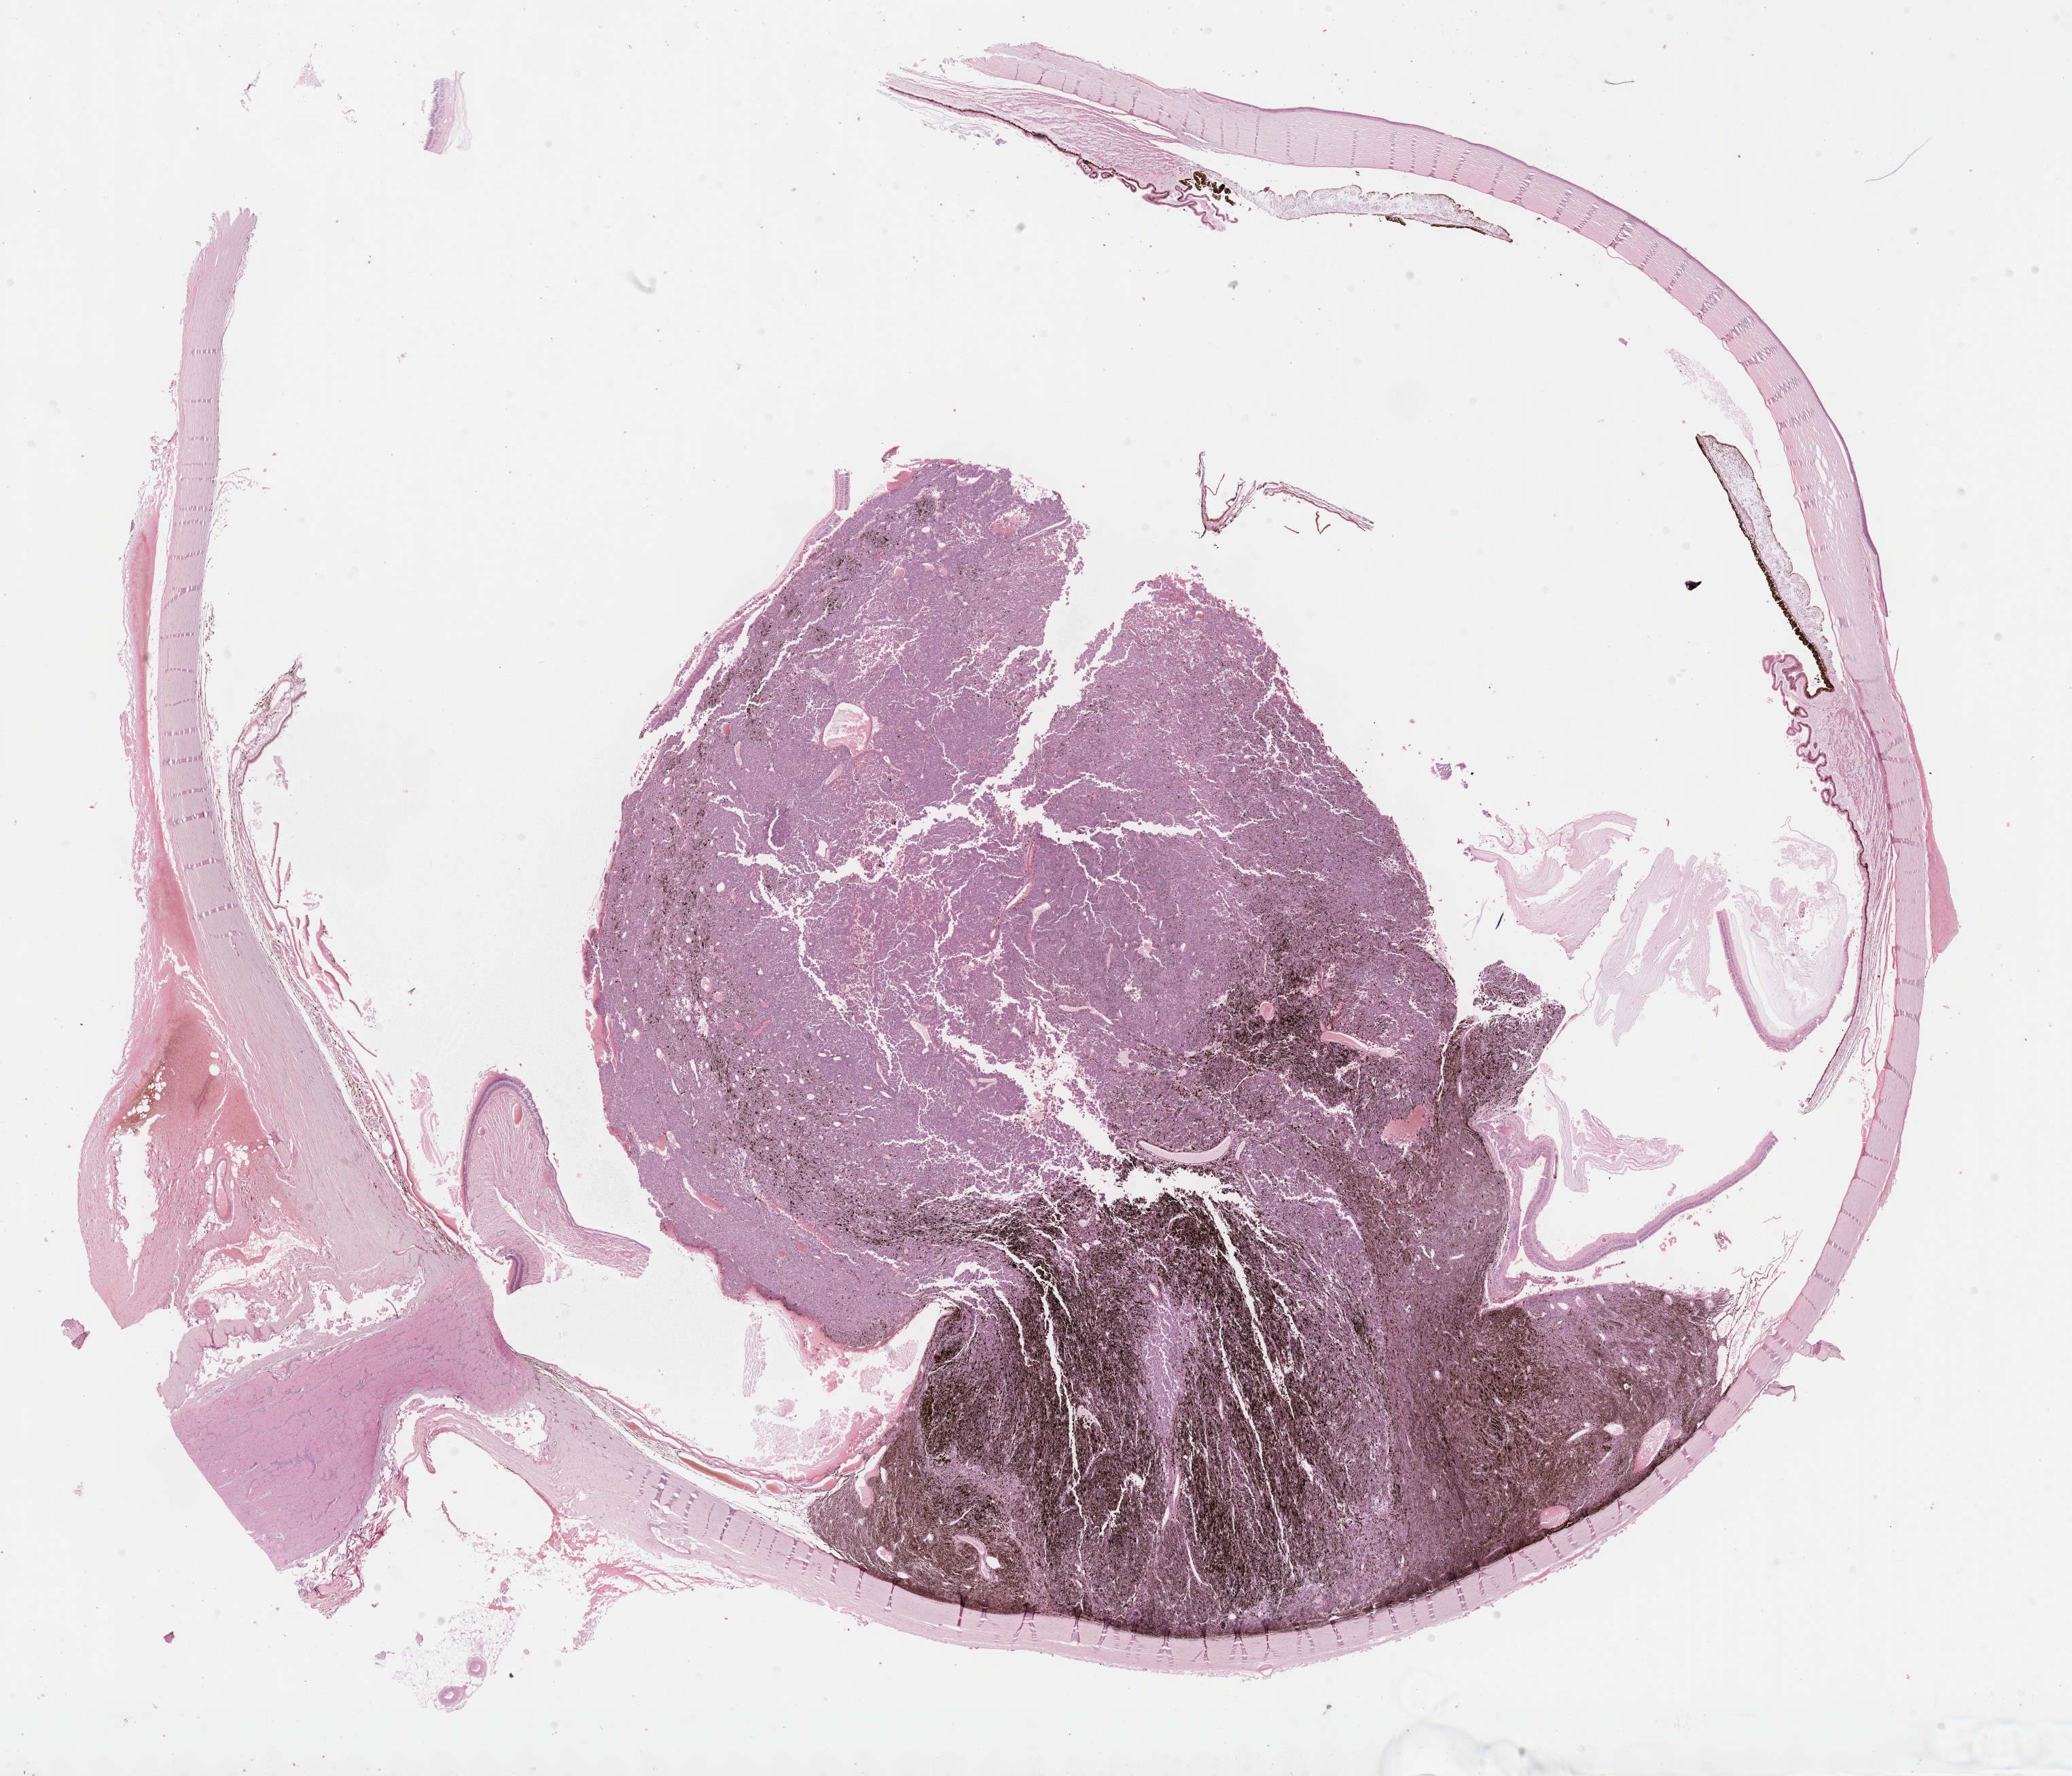
Whole-slide histology image, H&E-stained, shown as a low-resolution overview of the whole scanned area (about 24.7 x 21.1 mm, acquisition: 40x scan); FFPE section; sample: primary tumour, uvea. Female, age 55 years at initial diagnosis.
• histologic diagnosis: Epithelioid cell melanoma (choroid)
• AJCC pathologic stage: IIIA (7th edition)